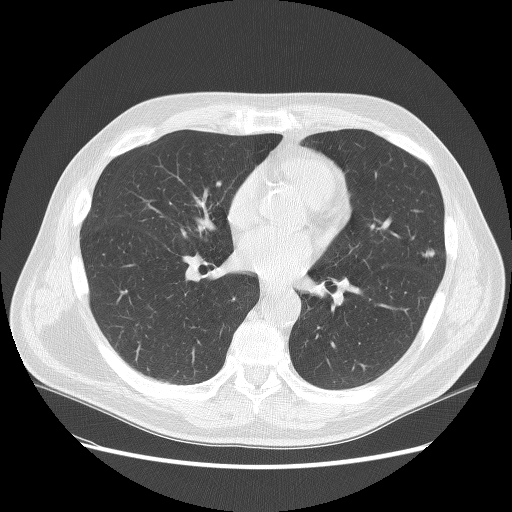
Chest CT (low-dose screening protocol), one axial image, second annual screen, lung window (W 1500 / L -600 HU). Male participant, aged 67 years at enrolment.
Expert-annotated lung lesion, bounding box <401,231,456,275> (left, top, right, bottom; pixels). Screening reader's record for this exam (one nodule recorded; not confirmed to be the boxed lesion): non-calcified nodule or mass ≥4 mm, left upper lobe, 10 × 6 mm, soft tissue attenuation, pre-existing on the prior screen: yes; interval growth: no. Lung cancer was diagnosed 393 days after this screen (after the third annual screen): squamous cell carcinoma, NOS, left upper lobe, moderately differentiated (G2), stage IB (AJCC 6th edition), 25 mm at pathology.